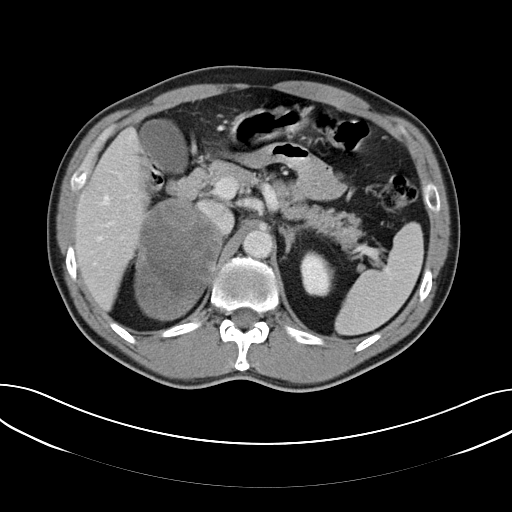
Contrast-enhanced abdominal CT, one axial slice. Slice 36 of 61 in the series (ordered by position). Soft-tissue window (W 400 / L 40 HU). 5 mm slice thickness. 512 × 512 image matrix, field of view 372 × 372 mm. Patient: male, 57 years. From the clinical record (not read from this slice): diagnosis: adrenocortical carcinoma; tumour side: right adrenal; tumour size at pathology: 11.2 cm; Ki-67 index: 10 %; stage (as recorded): 3.
Structures marked on this image (semi-automatic segmentation, software-assisted and operator-edited):
- mass: bounding box [x1, y1, x2, y2] px = [135, 201, 220, 319]